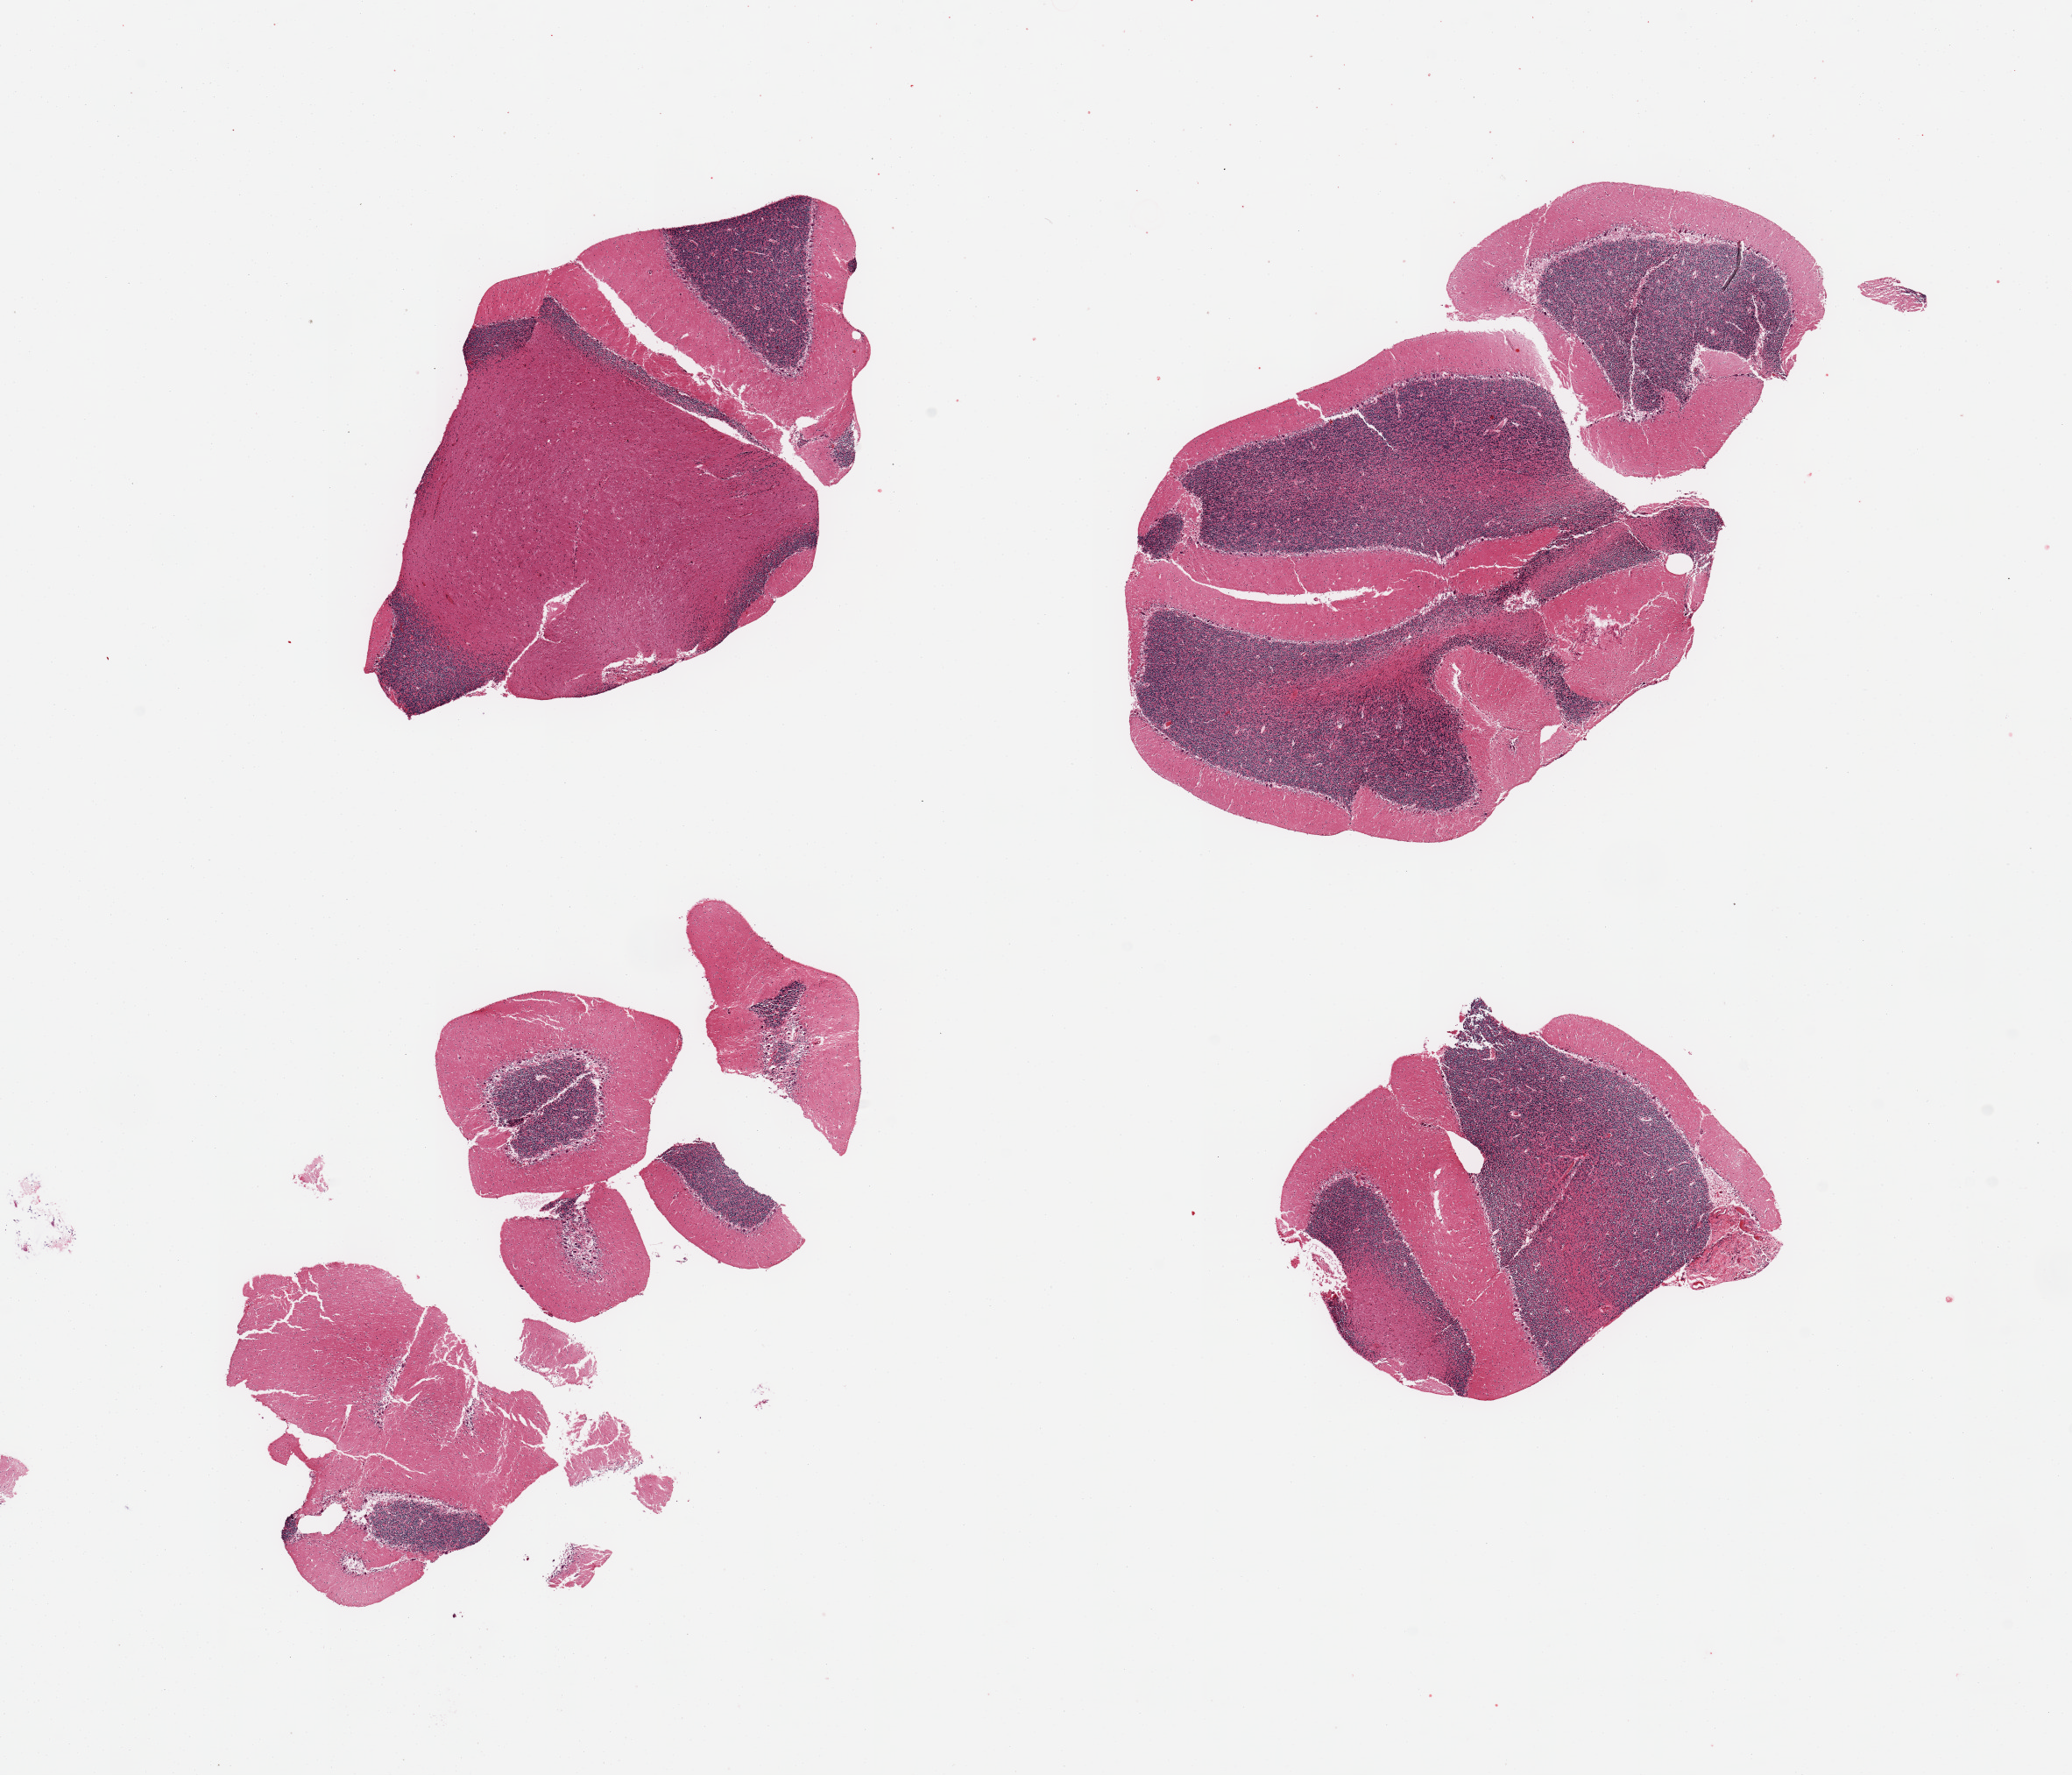
Whole-slide image, hematoxylin and eosin (H&E) stain, brightfield, a low-resolution overview of the entire scanned area, about 18.7 x 16.0 mm (acquisition: 20x scan), PAXgene-fixed, paraffin-embedded tissue, target tissue: cerebellum, tissue donor sample.
• pathologist's review note for this sample: 4 pieces, fragmented, no abnormalities